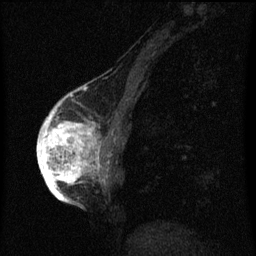
Breast MRI (dynamic contrast-enhanced), one sagittal slice. Position 22 of 60 along the scan axis. Dynamic contrast-enhanced series, image 2 of 3 at this slice position (ordered by acquisition). 1.5 T. TE 4.2 ms, TR 8 ms. 2 mm slice thickness. 256 × 256 image matrix. Patient: female, 56 years.
Outlined on this slice (semi-automatically segmented with operator editing):
- analysis volume of interest (the breast-tissue region the enhancement analysis was run in; not a lesion): bounding box (x1, y1, x2, y2) in pixels: (42, 110, 103, 193)
- tumour enhancement mask (voxels above the 70 % enhancement threshold inside the analysis volume of interest): (42, 110, 101, 193)